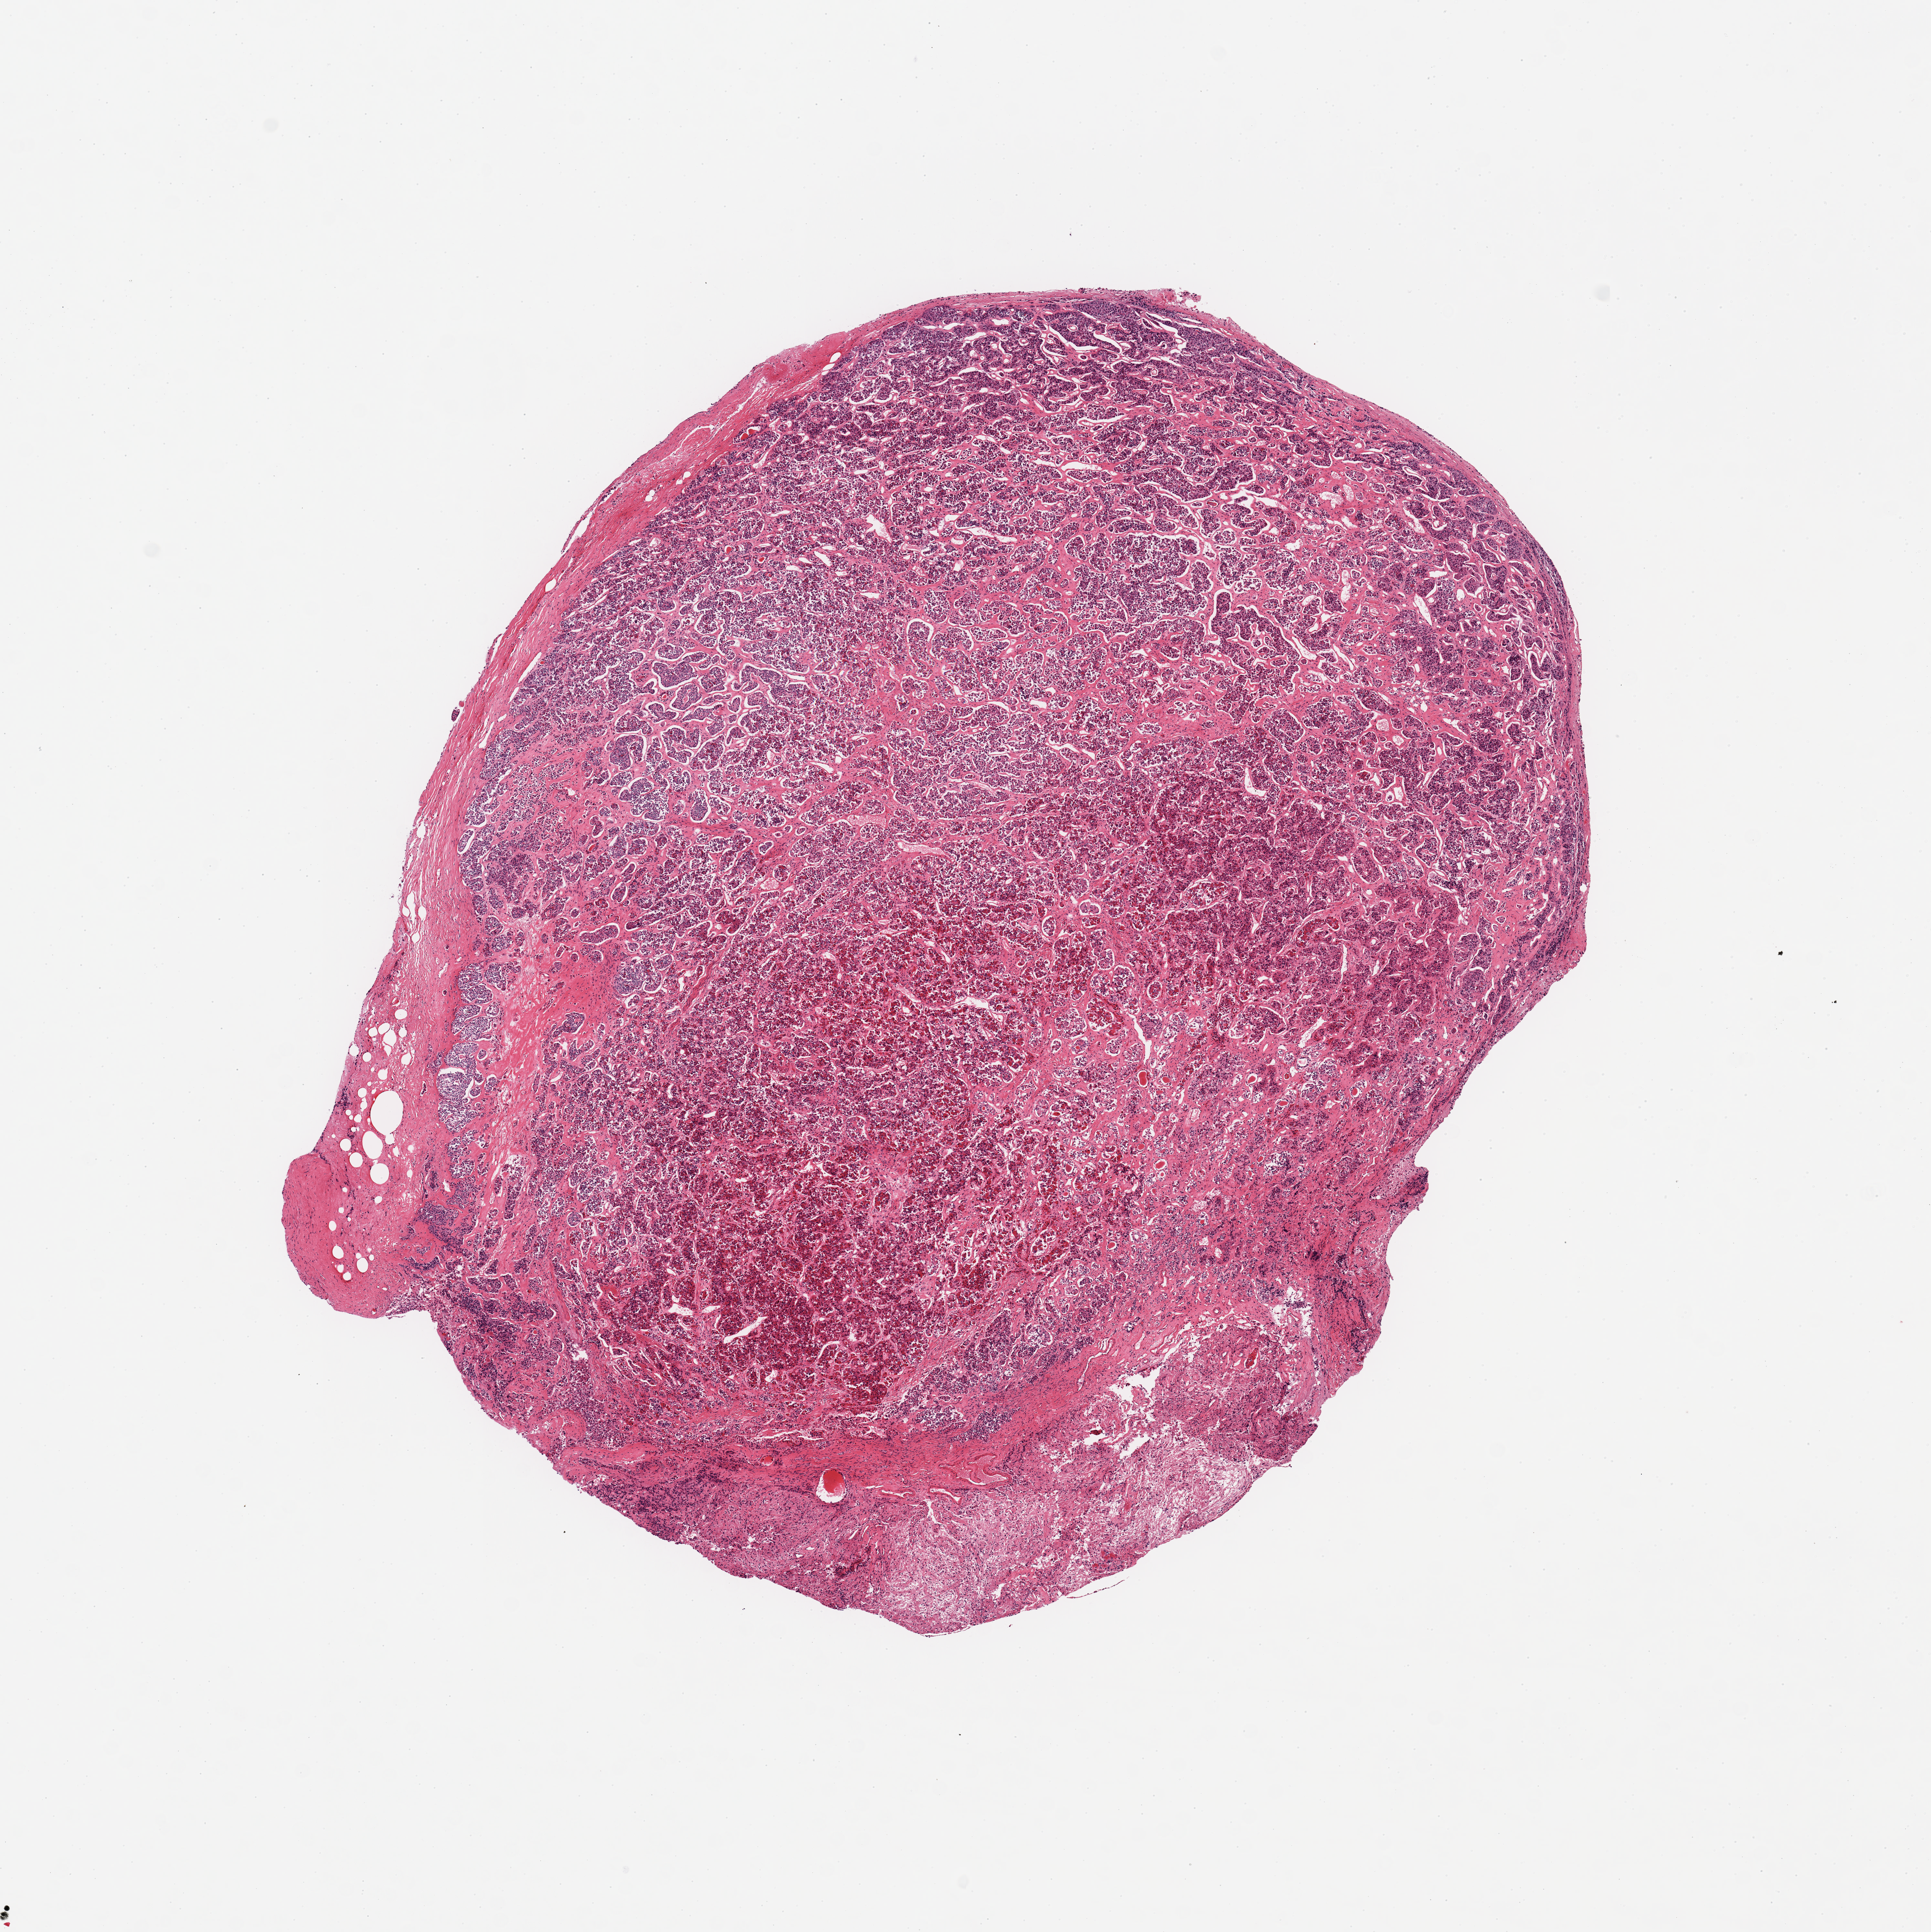
Digitized H&E-stained section — shown as a low-resolution overview of the whole scanned area (about 11.8 x 11.8 mm). PAXgene-fixed, paraffin-embedded tissue. Sampled site (target tissue): pituitary. Donor tissue sample. Donor: male.
Review note (as recorded): 1 piece; mainly adenohypophysis; ~3x1mm nubbin of neurohypophysis.